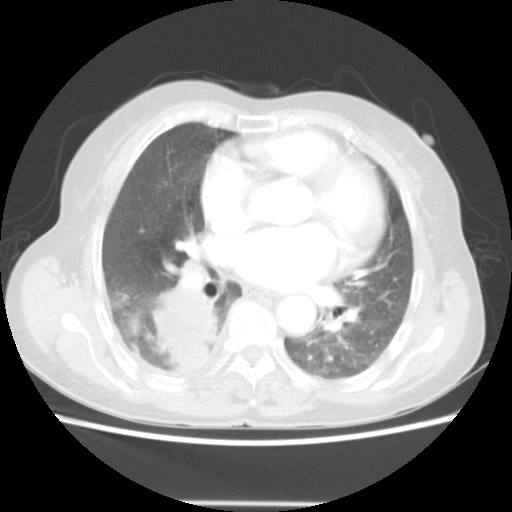
Chest CT, one axial slice; position 25 of 52 along the scan axis; reconstruction kernel STANDARD; 140 kVp; lung window (W 1500 / L -600 HU); 5 mm slice thickness; 512 × 512 image matrix, field of view 337 × 337 mm. Female patient, age 67 years. From the clinical record (not read from this slice): clinical TNM (as recorded): T3 N1 M1.
Outlined on this slice (rectangle marked by the reading radiologist):
- lung tumour (recorded histology: adenocarcinoma): bounding box [x1, y1, x2, y2] px = [147, 284, 219, 371]